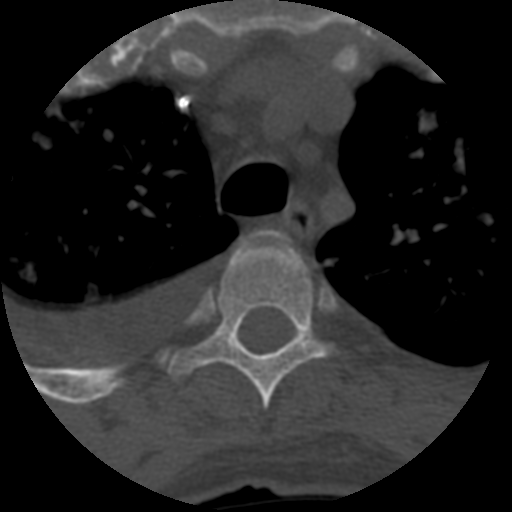
CT including the spine, one axial slice. Position 473 of 708 along the scan axis. Reconstruction kernel STANDARD. One of 3 acquisitions stored at this slice position. Bone window (W 1800 / L 400 HU). 512 × 512 image matrix, field of view 160 × 160 mm. Patient age 55 years. Case-level facts recorded for this patient, not image findings: primary cancer: colon; vertebrae with lytic lesions (as recorded): T12, L1, L5.
Structures marked on this image (semi-automatic segmentation, software-assisted and operator-edited):
- T3 vertebra: box from (x=253, y=231) to (x=274, y=239) px
- T4 vertebra: (x=169, y=236)–(x=339, y=410)